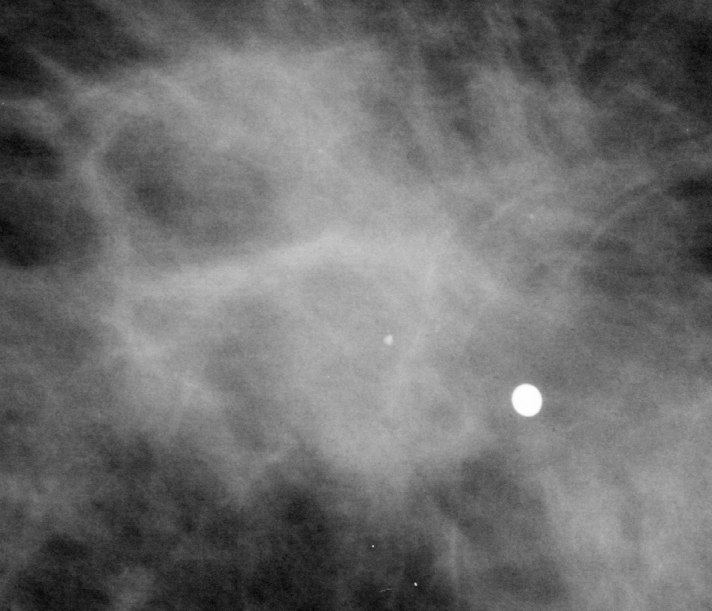
Crop from a digitized film mammogram around one marked abnormality; left breast; MLO view; BI-RADS breast density category 2 (scale 1–4).
Marked abnormality: mass, shape irregular, margins ill defined; BI-RADS assessment category 5; subtlety rating 5 on a 1 (subtle) to 5 (obvious) scale; pathology result (as recorded, not read from the image): malignant.